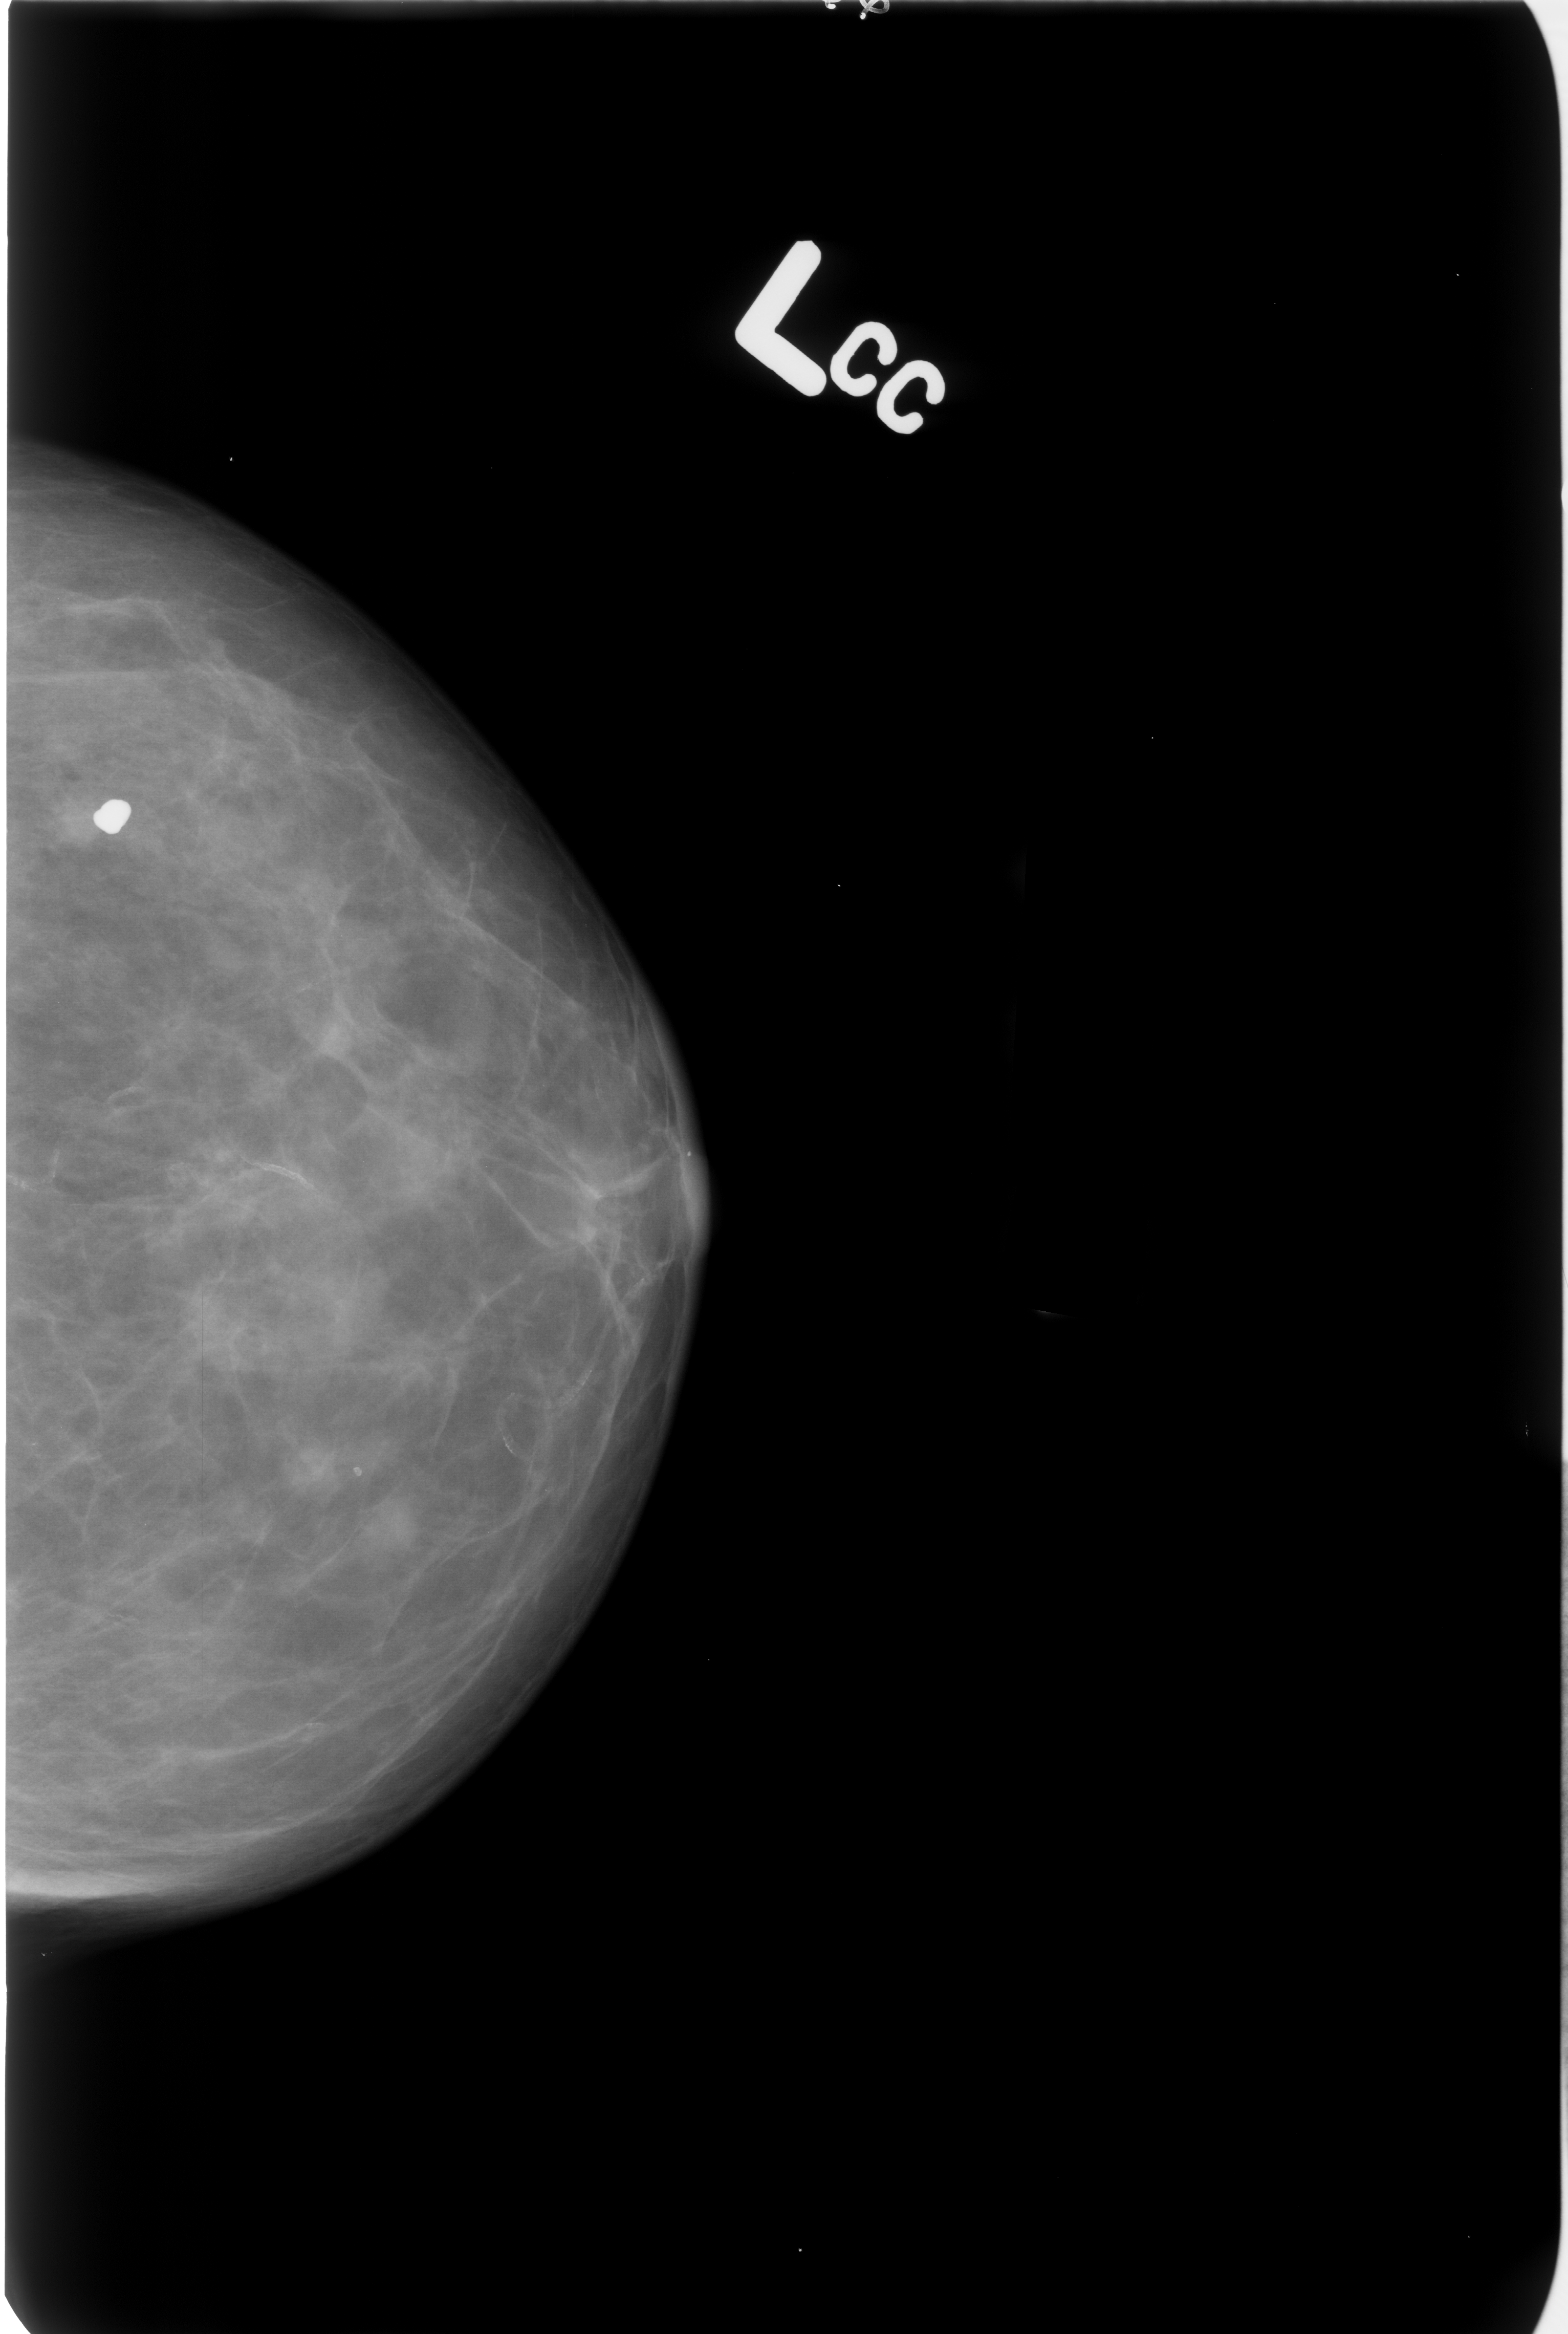
Mammogram (digitized film); left breast; CC view; BI-RADS breast density category 2 (scale 1–4); 1568 × 2334 image matrix.
Expert-marked regions of interest on this image (one box per marked abnormality):
- Finding 1 of 2: calcifications, morphology coarse; BI-RADS assessment category 2; subtlety rating 5 on a 1 (subtle) to 5 (obvious) scale; outcome (as recorded, no biopsy): benign without callback (not worked up further): bounding box (x1, y1, x2, y2) in pixels: (85, 790, 136, 840)
- Finding 2 of 2: calcifications, morphology vascular; BI-RADS assessment category 2; subtlety rating 5 on a 1 (subtle) to 5 (obvious) scale; outcome (as recorded, no biopsy): benign without callback (not worked up further): (491, 1207, 685, 1545)